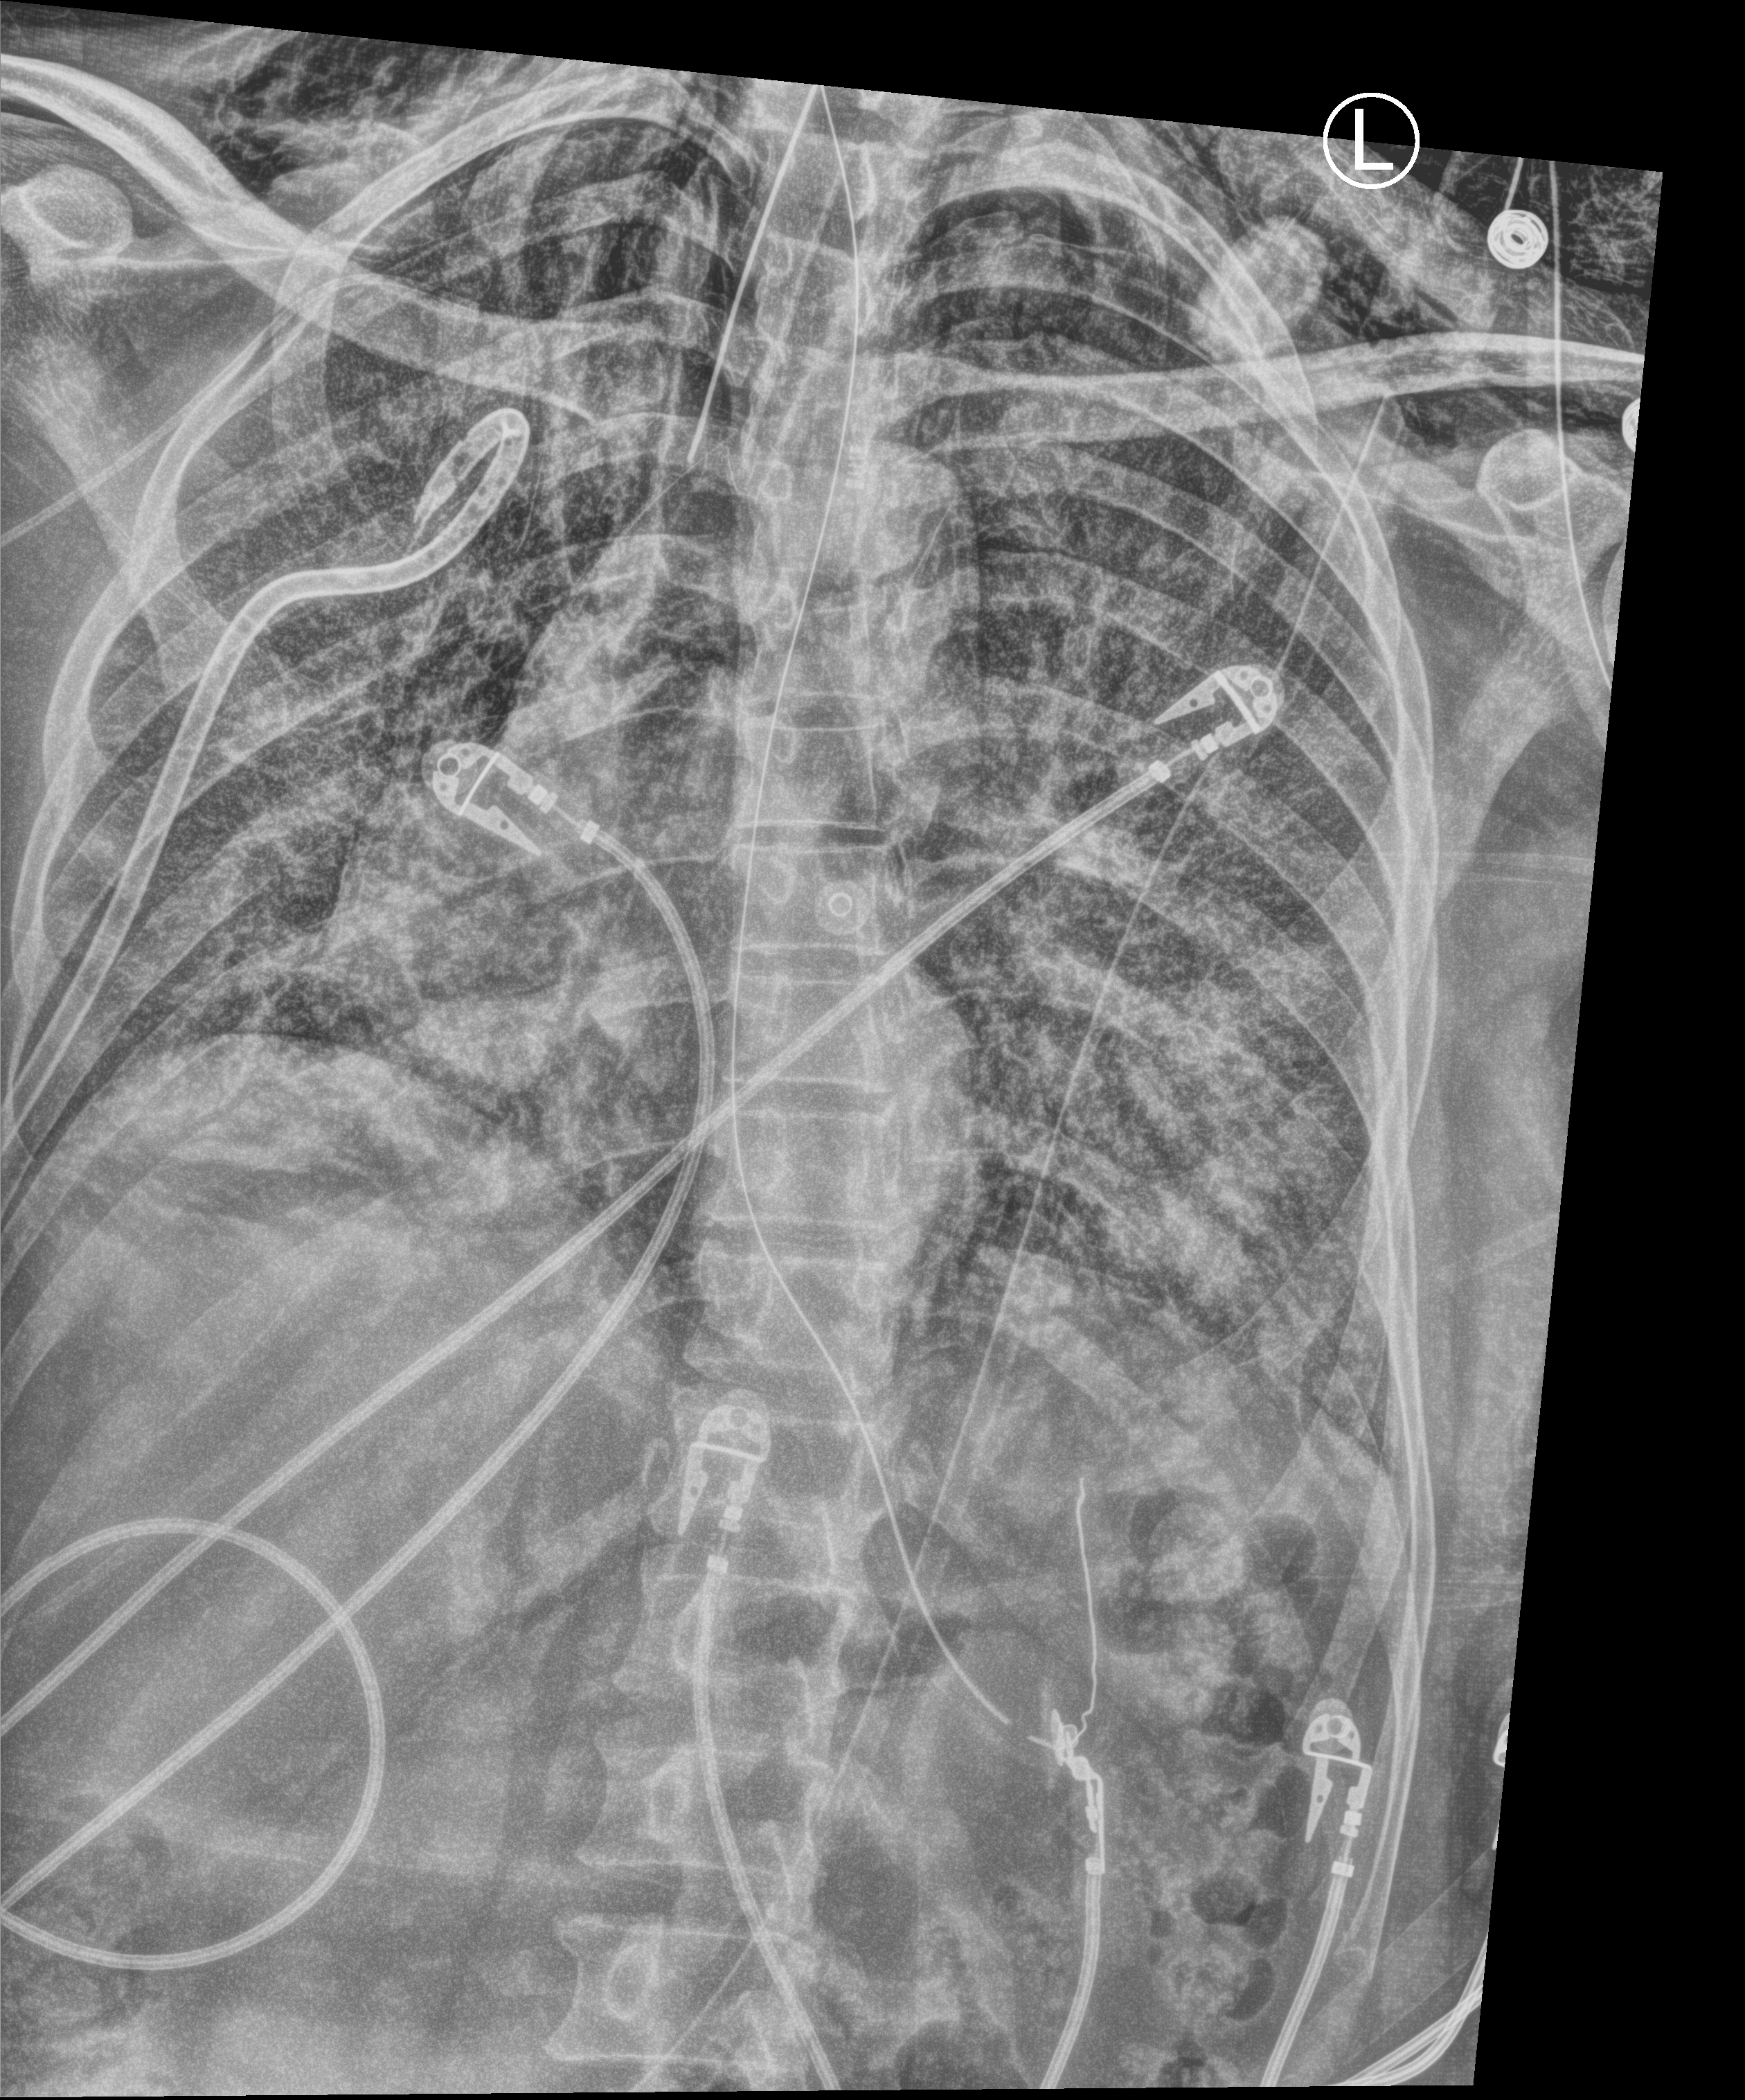
Bedside chest radiograph (computed radiography), anteroposterior (AP) projection. Patient hospitalised with COVID-19, aged 18–59 years.
Admission-level facts for this patient (not findings on this image; timing relative to this image not recorded): mechanically ventilated during this hospital stay: yes; admitted to intensive care during this hospital stay: yes; other chronic lung disease (admission record): no.